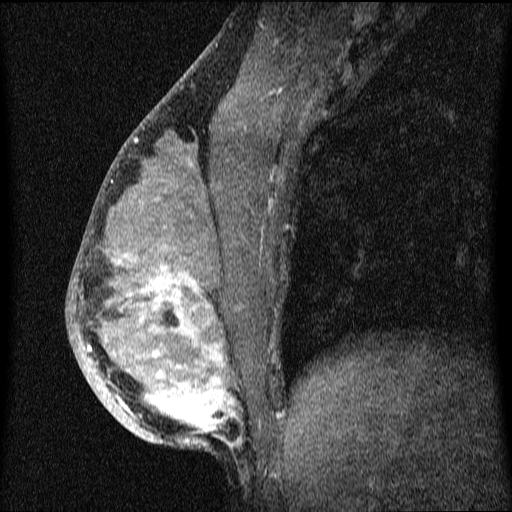
Breast MRI (dynamic contrast-enhanced), one sagittal slice. Slice 30 of 64 in the series (ordered by position). Dynamic contrast-enhanced series, image 2 of 4 at this slice position (ordered by acquisition). 1.5 T. TE 4.2 ms, TR 9.1 ms. 2 mm slice thickness. 512 × 512 image matrix, field of view 180 × 180 mm. Female patient, age 33 years.
Structures marked on this image (semi-automatically segmented with operator editing):
- analysis volume of interest (the breast-tissue region the enhancement analysis was run in; not a lesion): bounding box (x1, y1, x2, y2) in pixels: (67, 151, 336, 458)
- tumour enhancement mask (voxels above the 70 % enhancement threshold inside the analysis volume of interest): (89, 256, 237, 447)